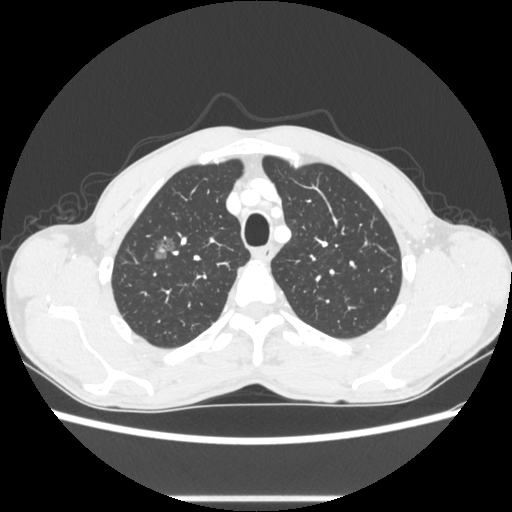
Chest CT, one axial slice; position 229 of 289 along the scan axis; reconstruction kernel STANDARD; 100 kVp; lung window (W 1500 / L -600 HU); 1.25 mm slice thickness; 512 × 512 image matrix, field of view 350 × 350 mm. Patient: male, 54 years. Case-level facts recorded for this patient, not image findings: clinical TNM (as recorded): T1a N0 M0.
Outlined on this slice (rectangle marked by the reading radiologist):
- lung tumour (recorded histology: adenocarcinoma): bounding box (x1, y1, x2, y2) in pixels: (146, 230, 180, 268)